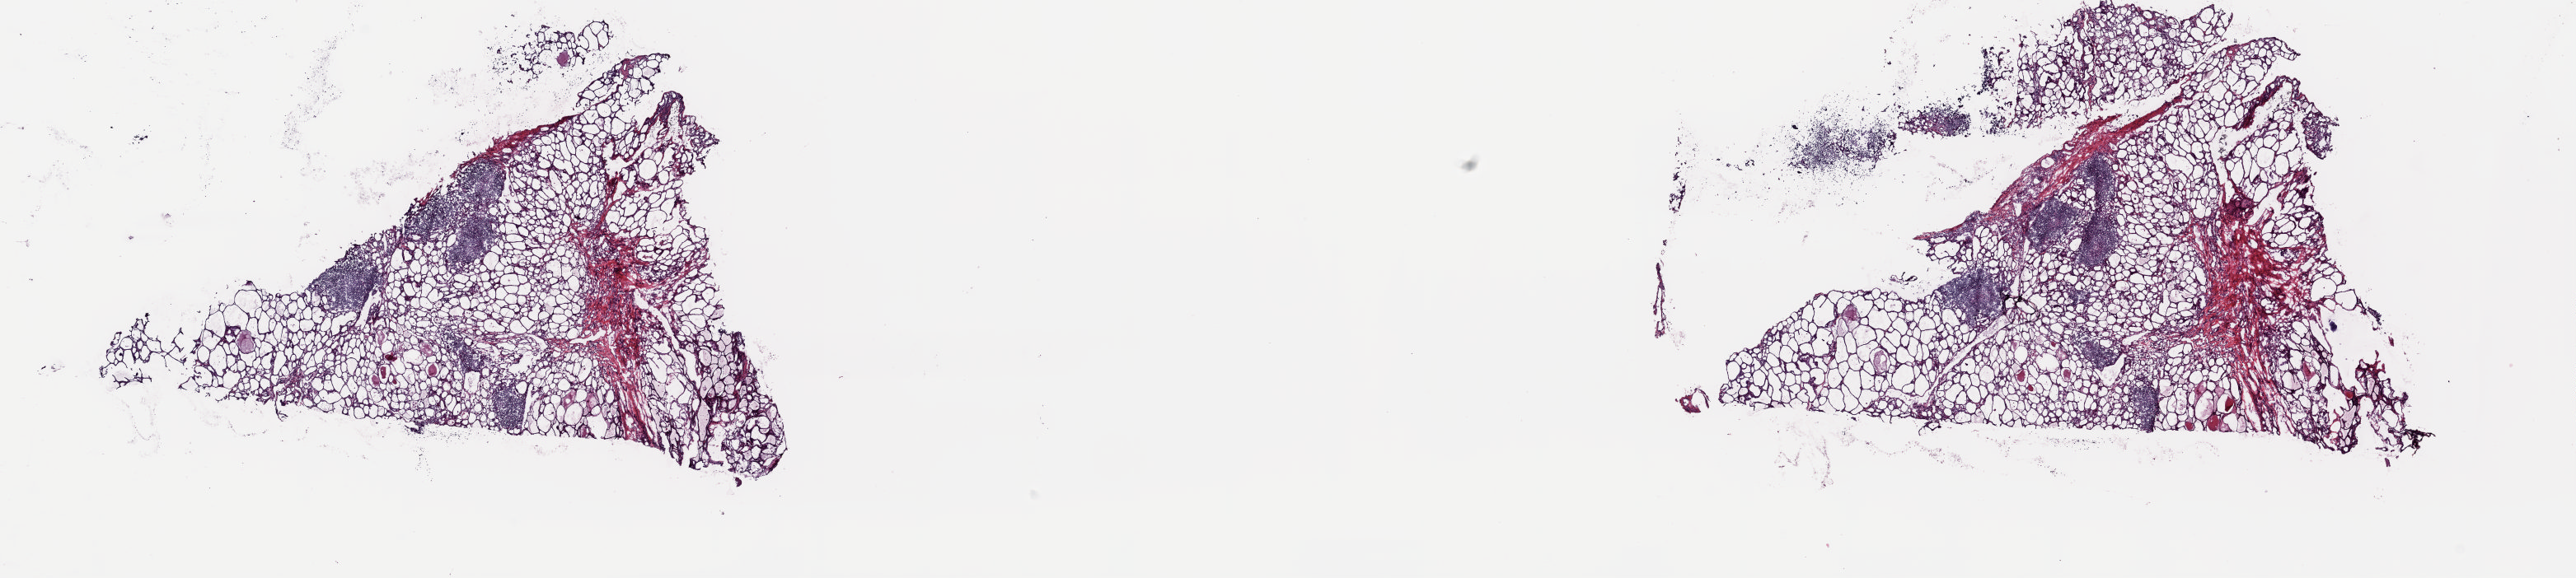
Hematoxylin and eosin (H&E) stained whole-slide image — low-resolution overview of the scanned area, about 24.8 x 5.6 mm; frozen section; solid tissue normal (non-tumour tissue) sample from the thyroid. Patient: female, age at initial diagnosis 47 years. Slide review estimates, as recorded: tumour cells 0%, tumour nuclei 0%, normal cells 100%, stromal cells 0%, necrosis 0%. Infiltration values recorded for this section: lymphocyte infiltration 10%, monocyte infiltration 4%, neutrophil infiltration 0%.
This section: solid tissue normal sample (biorepository sample class). Patient diagnosis: Papillary carcinoma, follicular variant (thyroid gland).